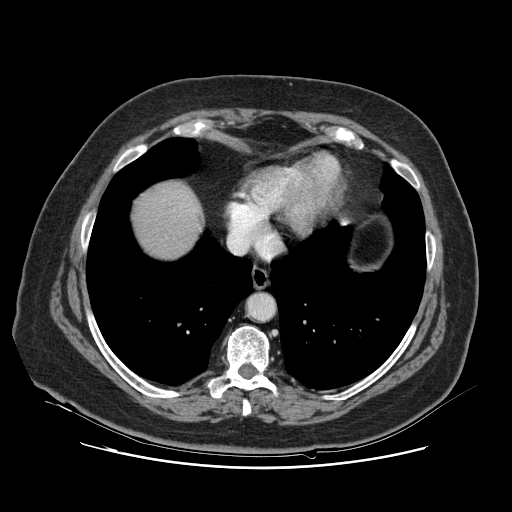
Contrast-enhanced abdominal CT, one axial slice. Slice 117 of 132 in the series (ordered by position). 120 kVp. Intravenous contrast given. Soft-tissue window (W 400 / L 40 HU). 512 × 512 image matrix, field of view 391 × 391 mm. Female patient, age 73 years. From the clinical record (not read from this slice): diagnosis: colorectal cancer liver metastases, imaged before liver resection; multiple liver metastases: no; largest metastasis: 7 cm; disease in both lobes: no.
Outlined on this slice (expert manual segmentation):
- liver: bounding box <132,183,198,260> (left, top, right, bottom; pixels)
- planned liver remnant (the part of the liver to remain after resection): <133,183,198,259>